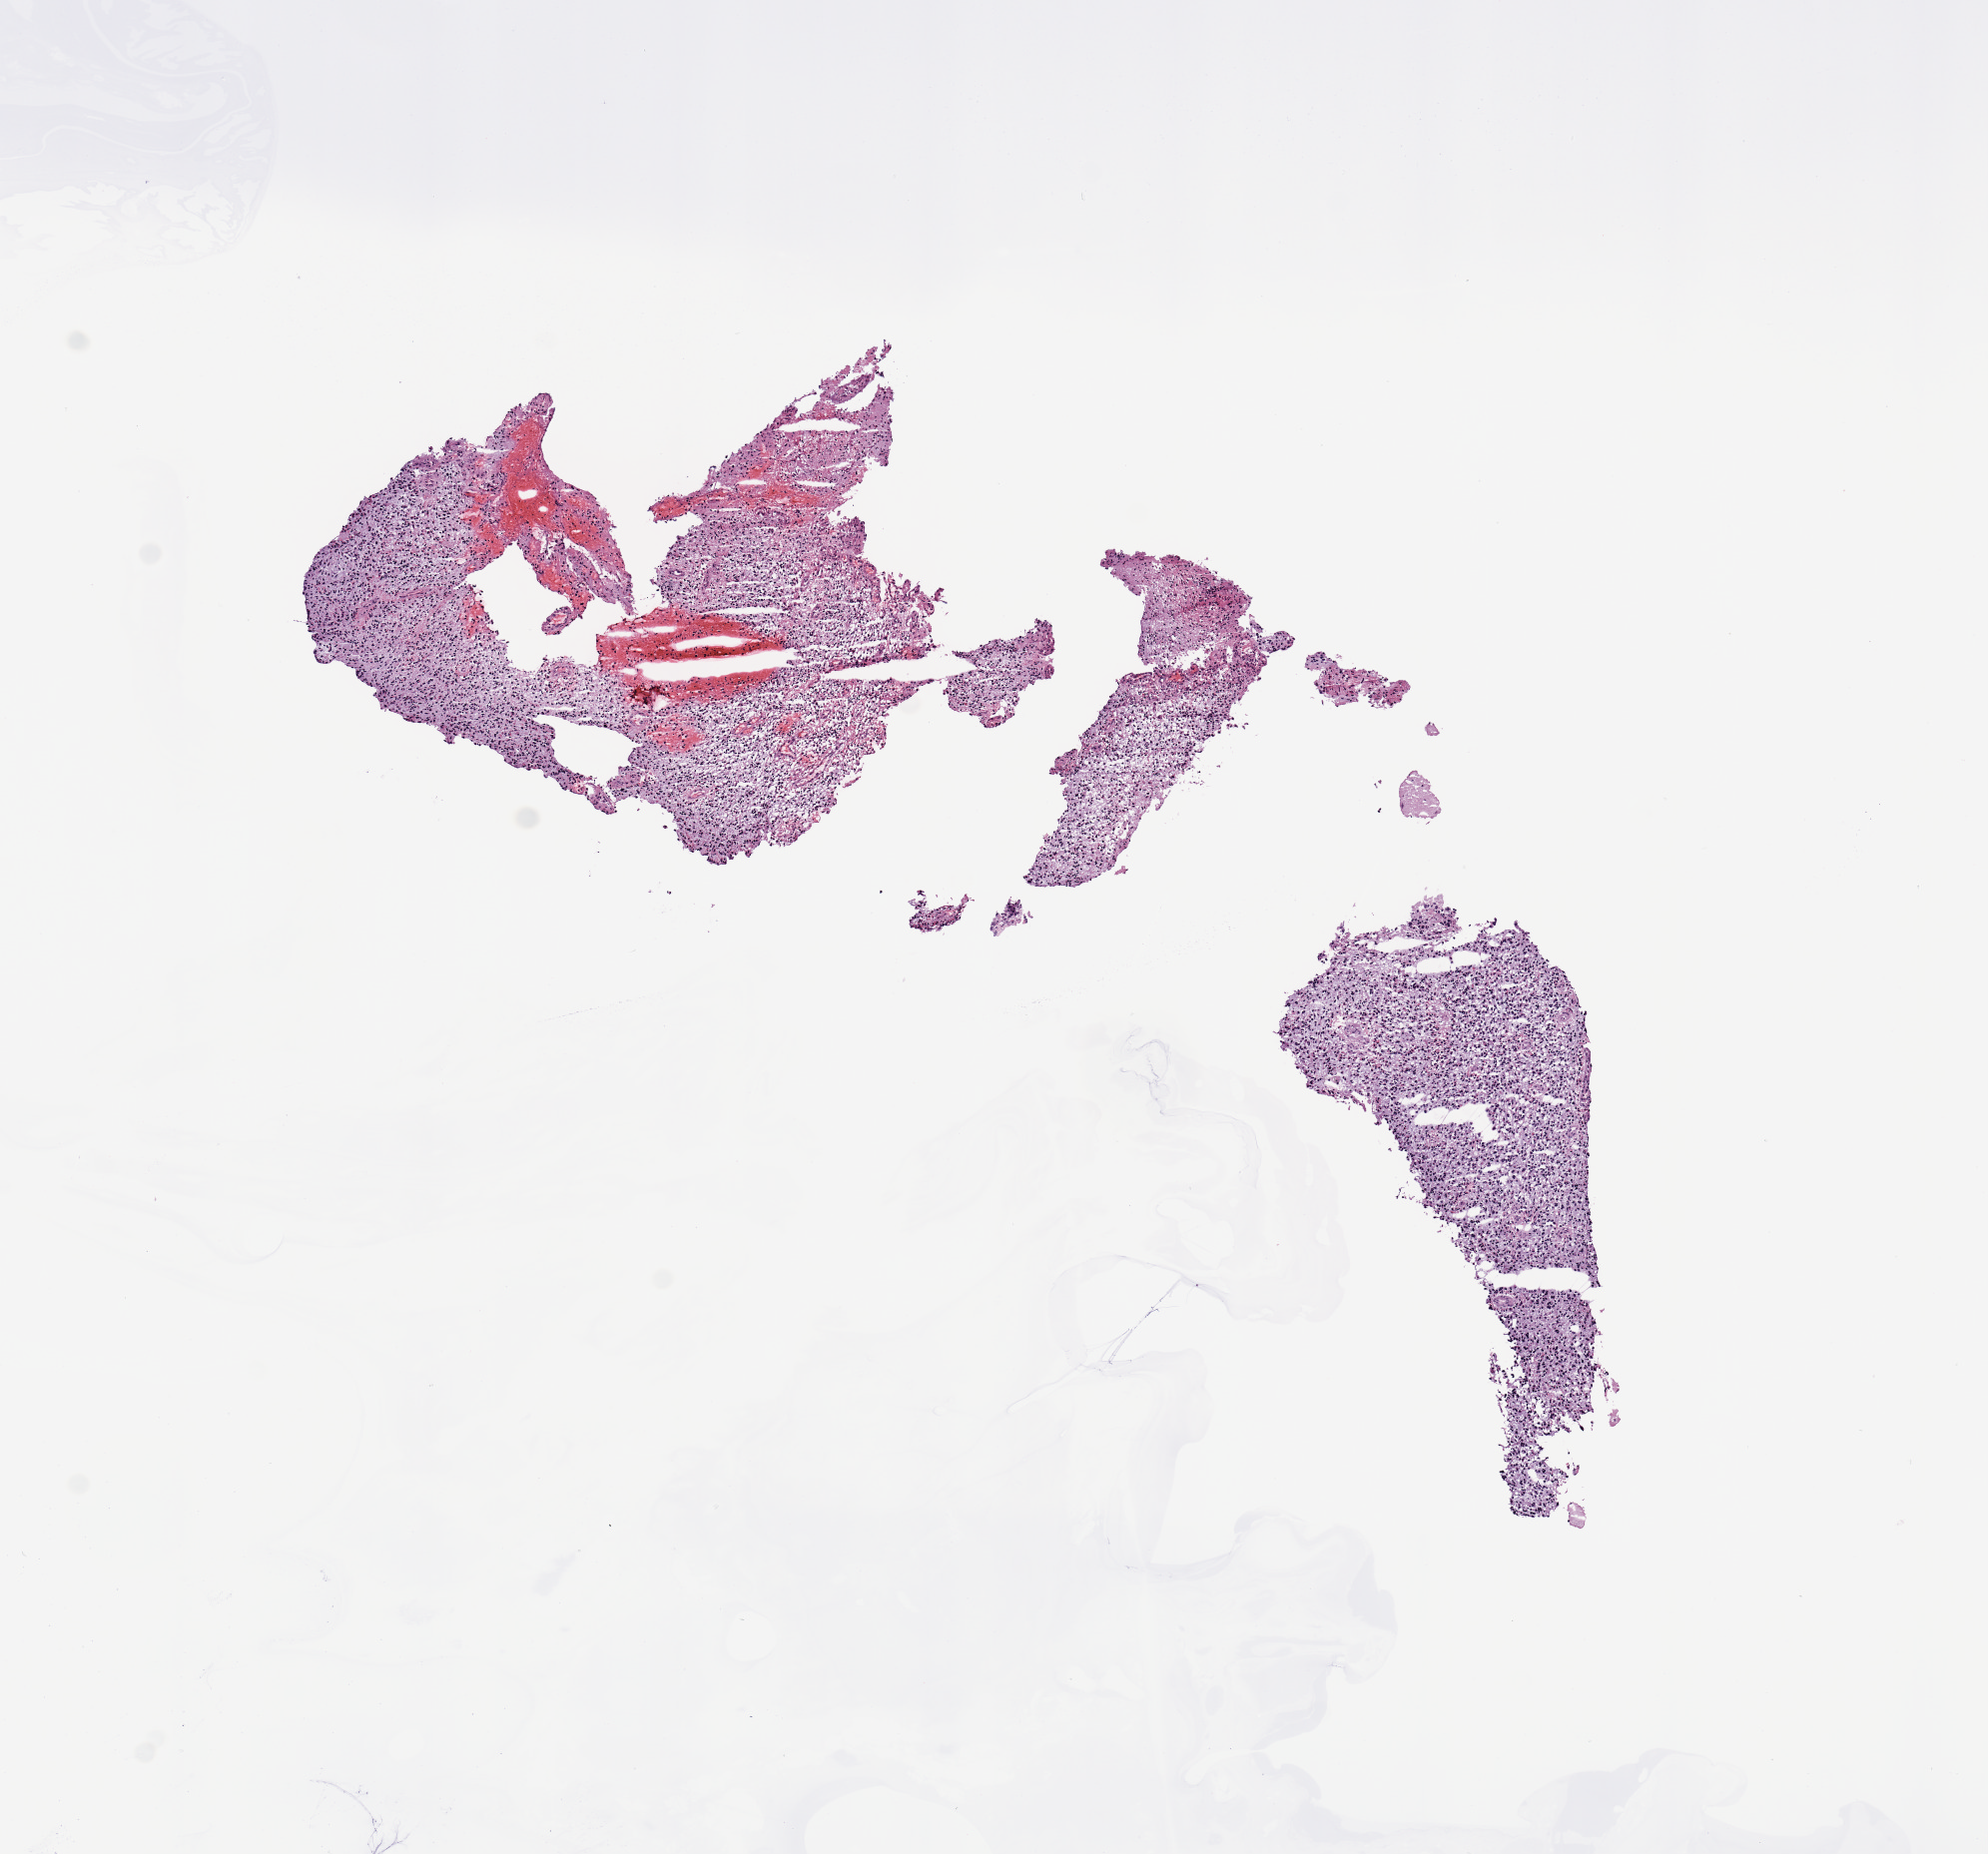
Hematoxylin and eosin (H&E) stained whole-slide image, low-resolution overview of the scanned area, about 7.9 x 7.3 mm (slide scanned at 20x). Brain, tumour tissue. Male, 61 y/o.
Patient diagnosis (cohort enrolment): glioblastoma multiforme (brain). Primary tumour site (as recorded): temporal lobe.